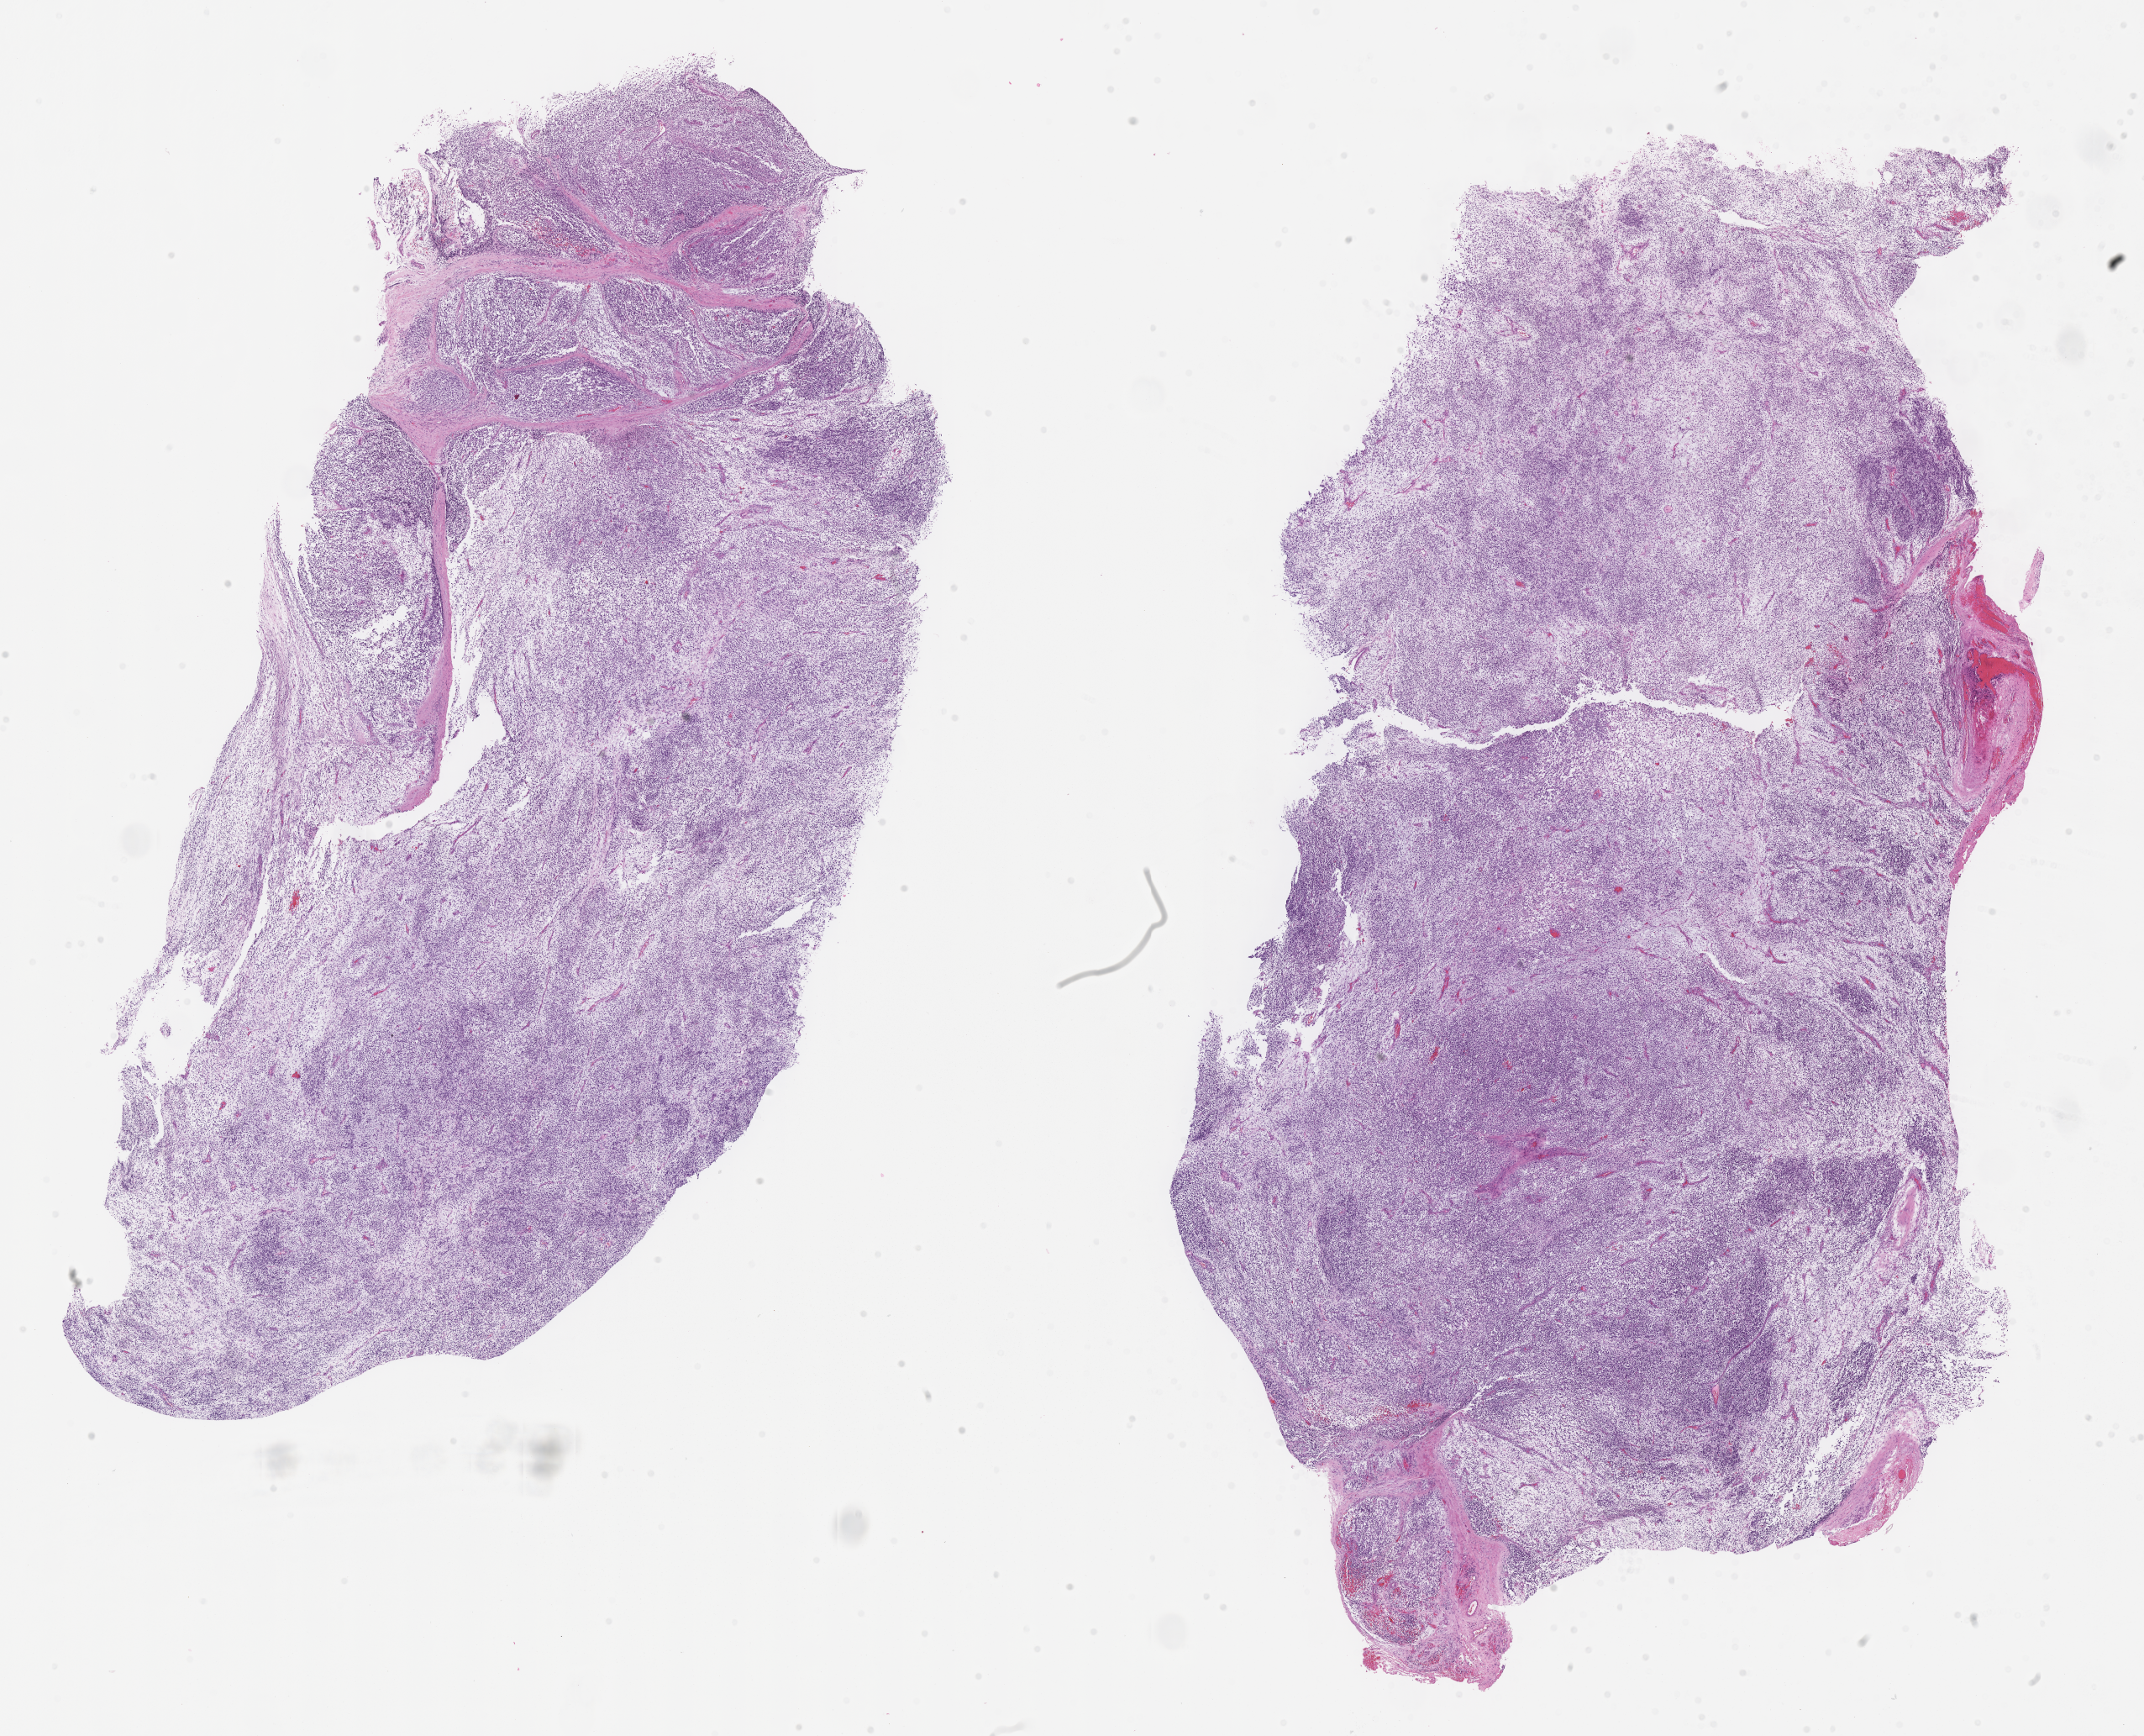
H&E whole-slide image of tumor tissue, shown as a low-resolution overview of the whole scanned area (about 20.6 x 16.7 mm); FFPE section; site: orbit, left. Male patient, age at diagnosis 8.4 years.
Diagnosis: rhabdomyosarcoma; histological classification: embryonal rhabdomyosarcoma. Metastatic status at presentation (as recorded): non-metastatic. Stage (as recorded): 1.